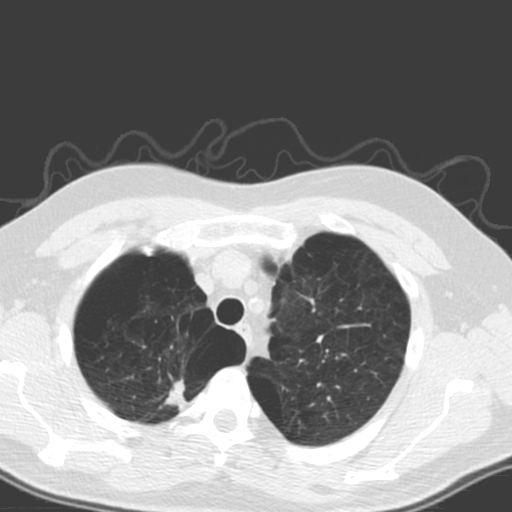
Low-dose screening chest CT, axial slice, baseline screening round, lung window (W 1500 / L -600 HU), 3.2 mm slice thickness, slice 33 of 173 in the series. Male, age 56 years at enrolment.
- Lesion marked by an expert reader, bounding box [x1, y1, x2, y2] px = [140, 354, 209, 430].
- The exam's reader record, not a measurement of the box and not confirmed to be the same lesion: non-calcified nodule or mass ≥4 mm, right upper lobe, 20 × 12 mm, spiculated (stellate) margins, soft tissue attenuation.
- Lung cancer was diagnosed 205 days after this screen: large cell carcinoma, NOS, right upper lobe, poorly differentiated (G3), stage IA (AJCC 6th edition), 18 mm at pathology.